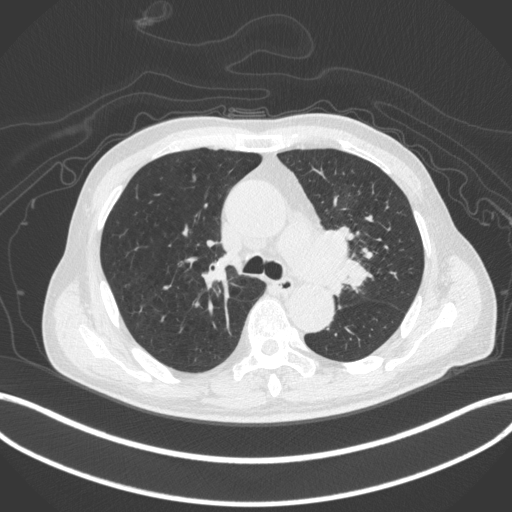
Chest CT, one axial slice; position 286 of 420 along the scan axis; reconstruction kernel B31f; 120 kVp; lung window (W 1500 / L -600 HU); 1 mm slice thickness; 512 × 512 image matrix, field of view 400 × 400 mm. Patient: male, 77 years. From the clinical record (not read from this slice): clinical TNM (as recorded): T3 N1 M0.
Annotated regions visible in this slice (bounding box drawn by a radiologist):
- lung tumour (recorded histology: adenocarcinoma): bounding box (x1, y1, x2, y2) in pixels: (311, 224, 374, 296)